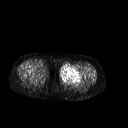
FDG PET of an extremity soft-tissue mass (from a PET/CT study), one axial slice; slice 235 of 267 in the series (ordered by position); 3.27 mm slice thickness; 128 × 128 image matrix, field of view 500 × 500 mm. Patient: female, 42 years. Case-level facts recorded for this patient, not image findings: histological type: pleiomorphic leiomyosarcoma; grade: intermediate; site of the primary tumour: left thigh.
Annotated regions visible in this slice (expert contour drawn on MRI and transferred to this co-registered scan by the dataset authors):
- gross tumour volume including surrounding oedema: bounding box <59,65,83,84> (left, top, right, bottom; pixels)
- gross tumour volume (mass): <59,65,82,83>